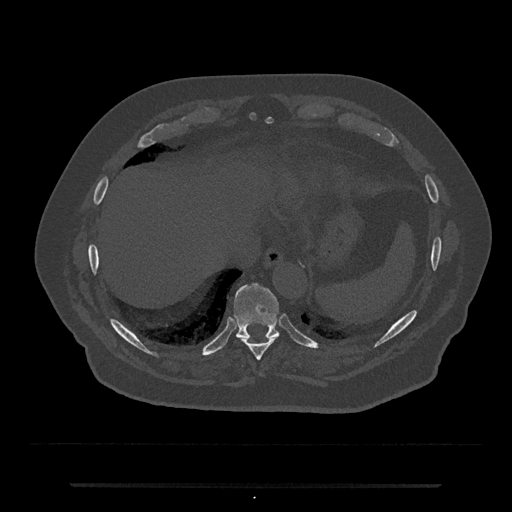
CT including the spine, one axial slice; slice 733 of 797 in the series (ordered by position); 120 kVp; bone window (W 1800 / L 400 HU); 0.5 mm slice thickness; 512 × 512 image matrix, field of view 434 × 434 mm. Male patient, age 80 years. From the clinical record (not read from this slice): primary cancer: prostate.
Annotated regions visible in this slice (semi-automatic segmentation, software-assisted and operator-edited):
- T10 vertebra: bounding box <234,283,280,338> (left, top, right, bottom; pixels)
- T9 vertebra: <240,337,277,361>